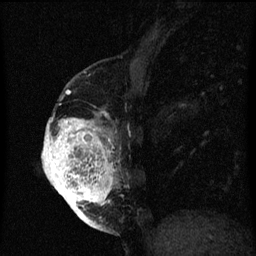
Breast MRI (dynamic contrast-enhanced), one sagittal slice; slice 21 of 60 in the series (ordered by position); dynamic contrast-enhanced series, image 2 of 3 at this slice position (ordered by acquisition); 1.5 T; TE 4.2 ms, TR 8 ms; 2 mm slice thickness; 256 × 256 image matrix. Female patient, age 56 years.
Outlined on this slice (semi-automatically segmented with operator editing):
- analysis volume of interest (the breast-tissue region the enhancement analysis was run in; not a lesion): bounding box <42,98,123,219> (left, top, right, bottom; pixels)
- tumour enhancement mask (voxels above the 70 % enhancement threshold inside the analysis volume of interest): <42,112,115,219>